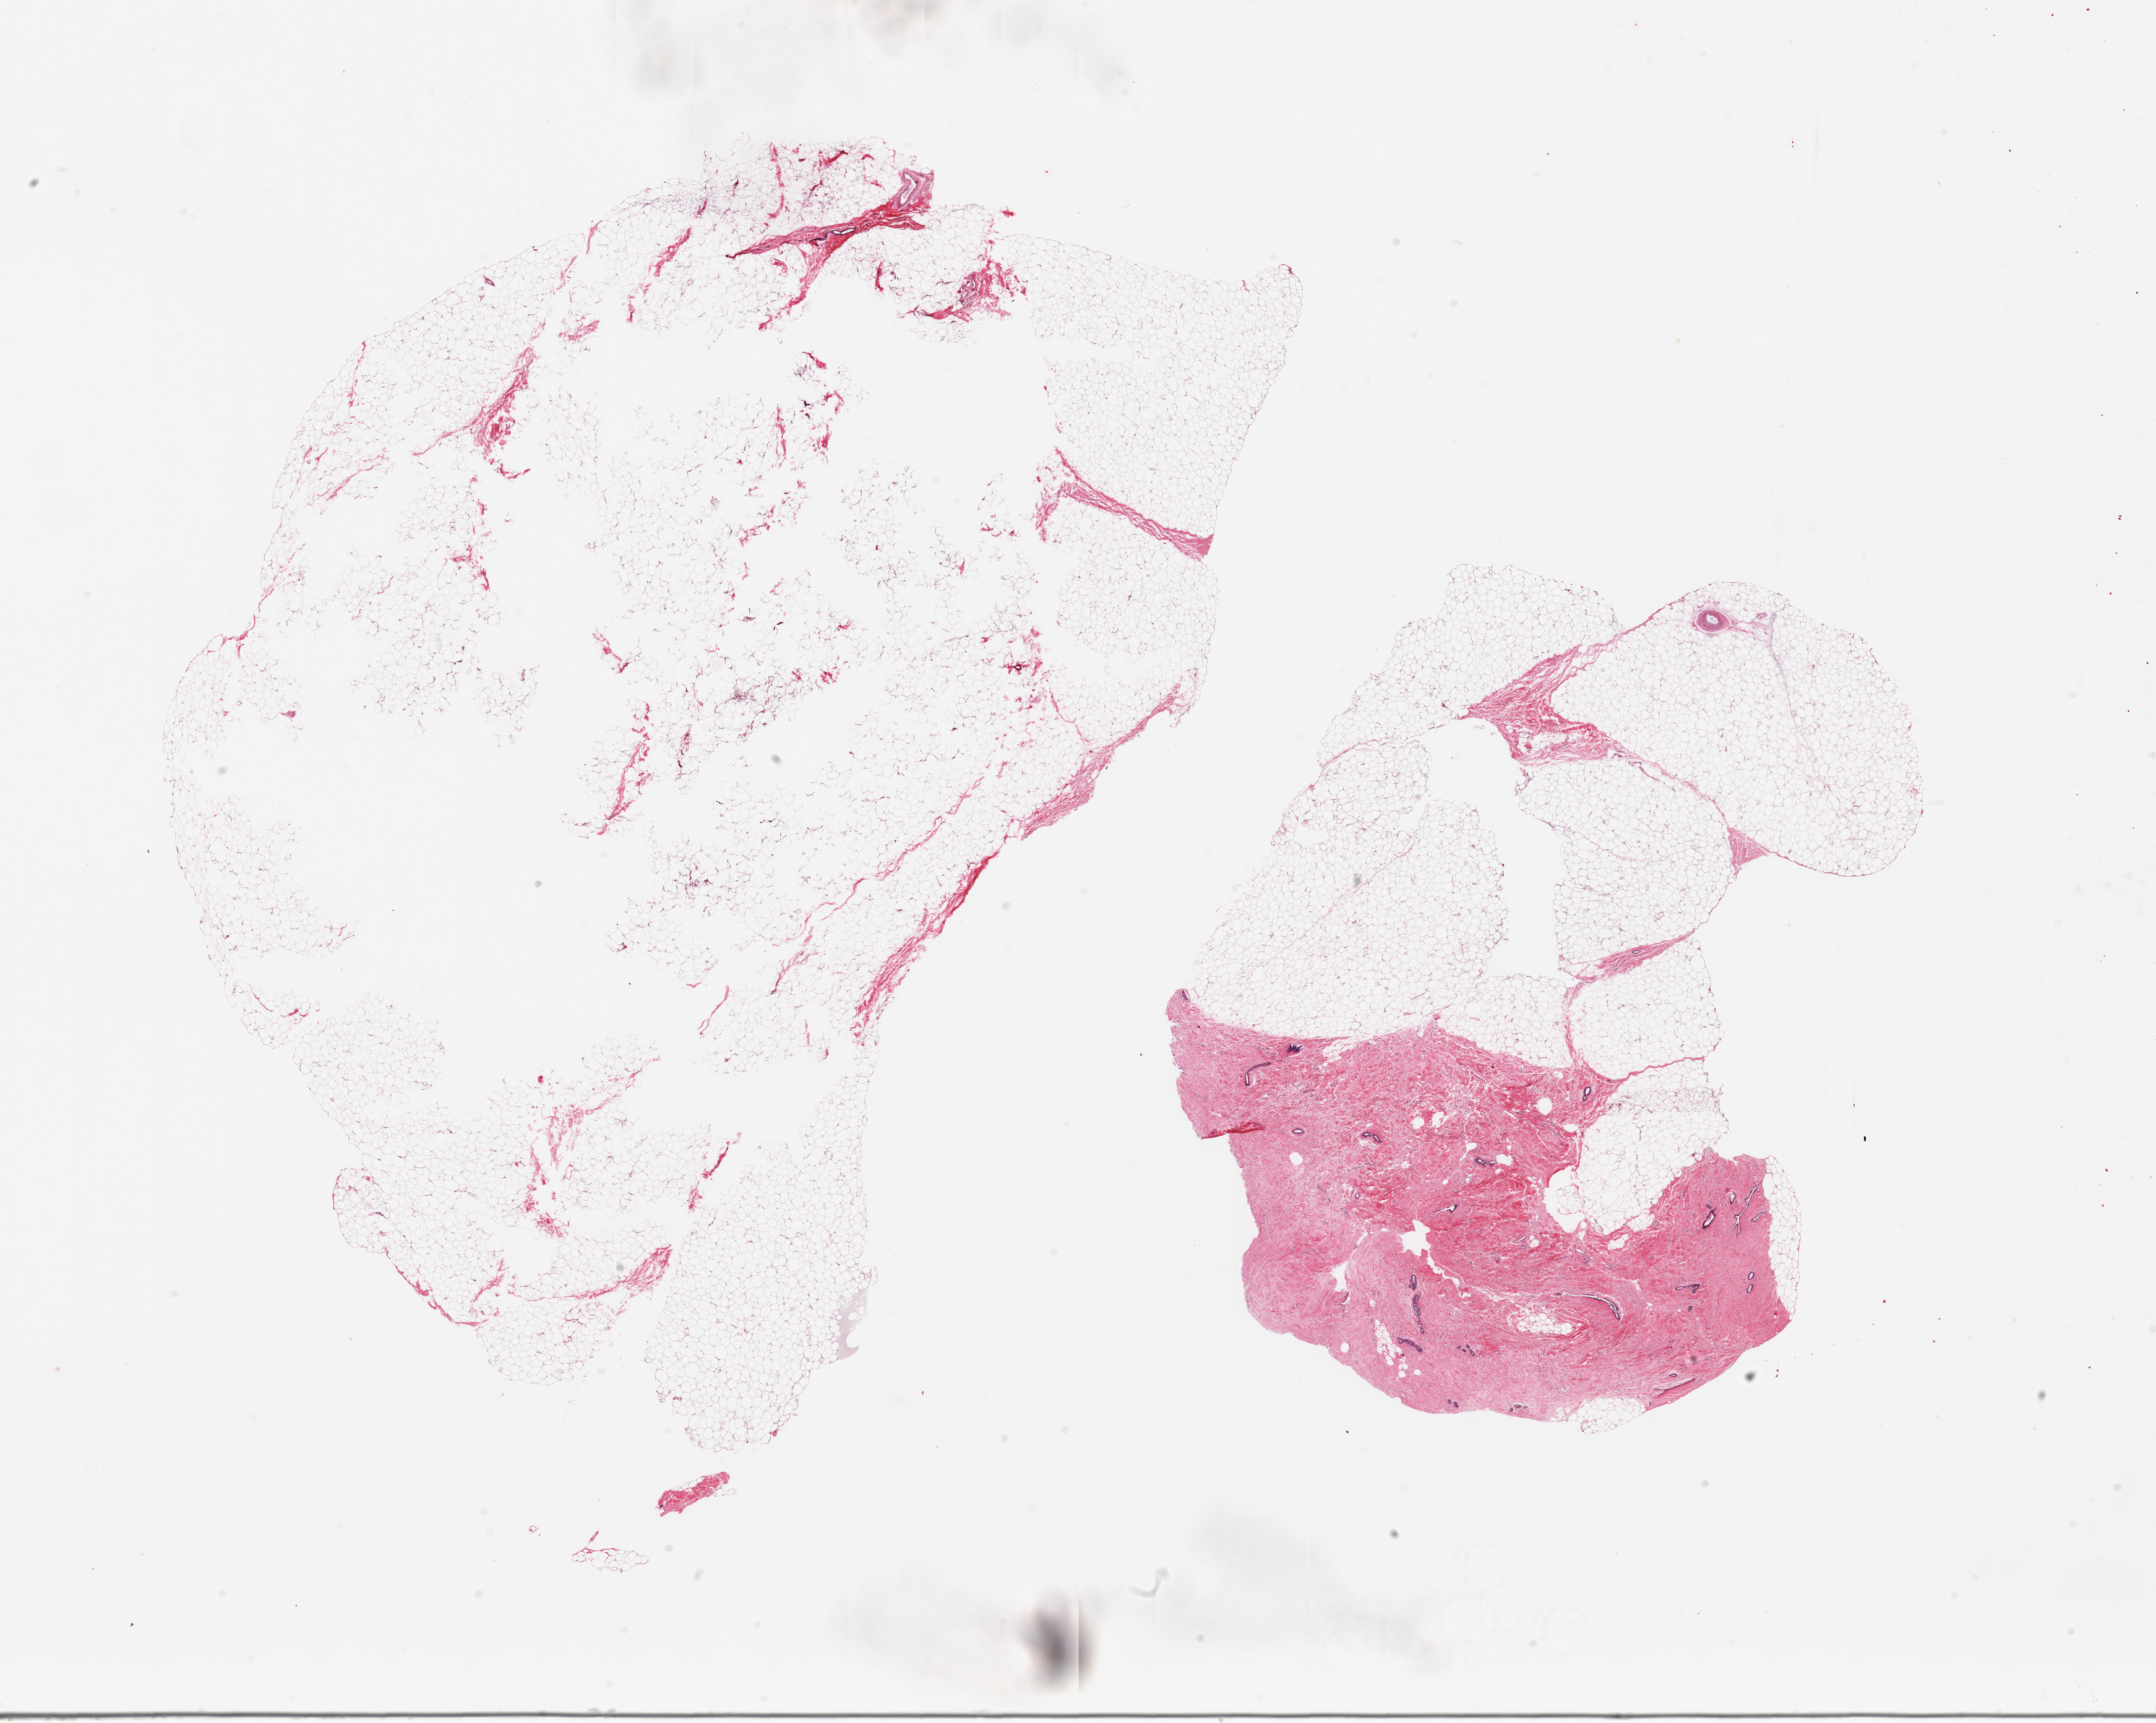
Digitized haematoxylin and eosin-stained section, shown as a low-resolution overview of the whole scanned area (about 27.6 x 22.0 mm, acquisition: 20x scan); PAXgene-fixed, paraffin-embedded tissue; target tissue: breast; tissue donor sample. Male donor.
* pathologist's review note for this sample: 2 pieces; predominantly mature adipose tissue, over-sized specimens with central defect (?poor fixation), one piece is 40% dense fibrous stroma with scattered ductal structures